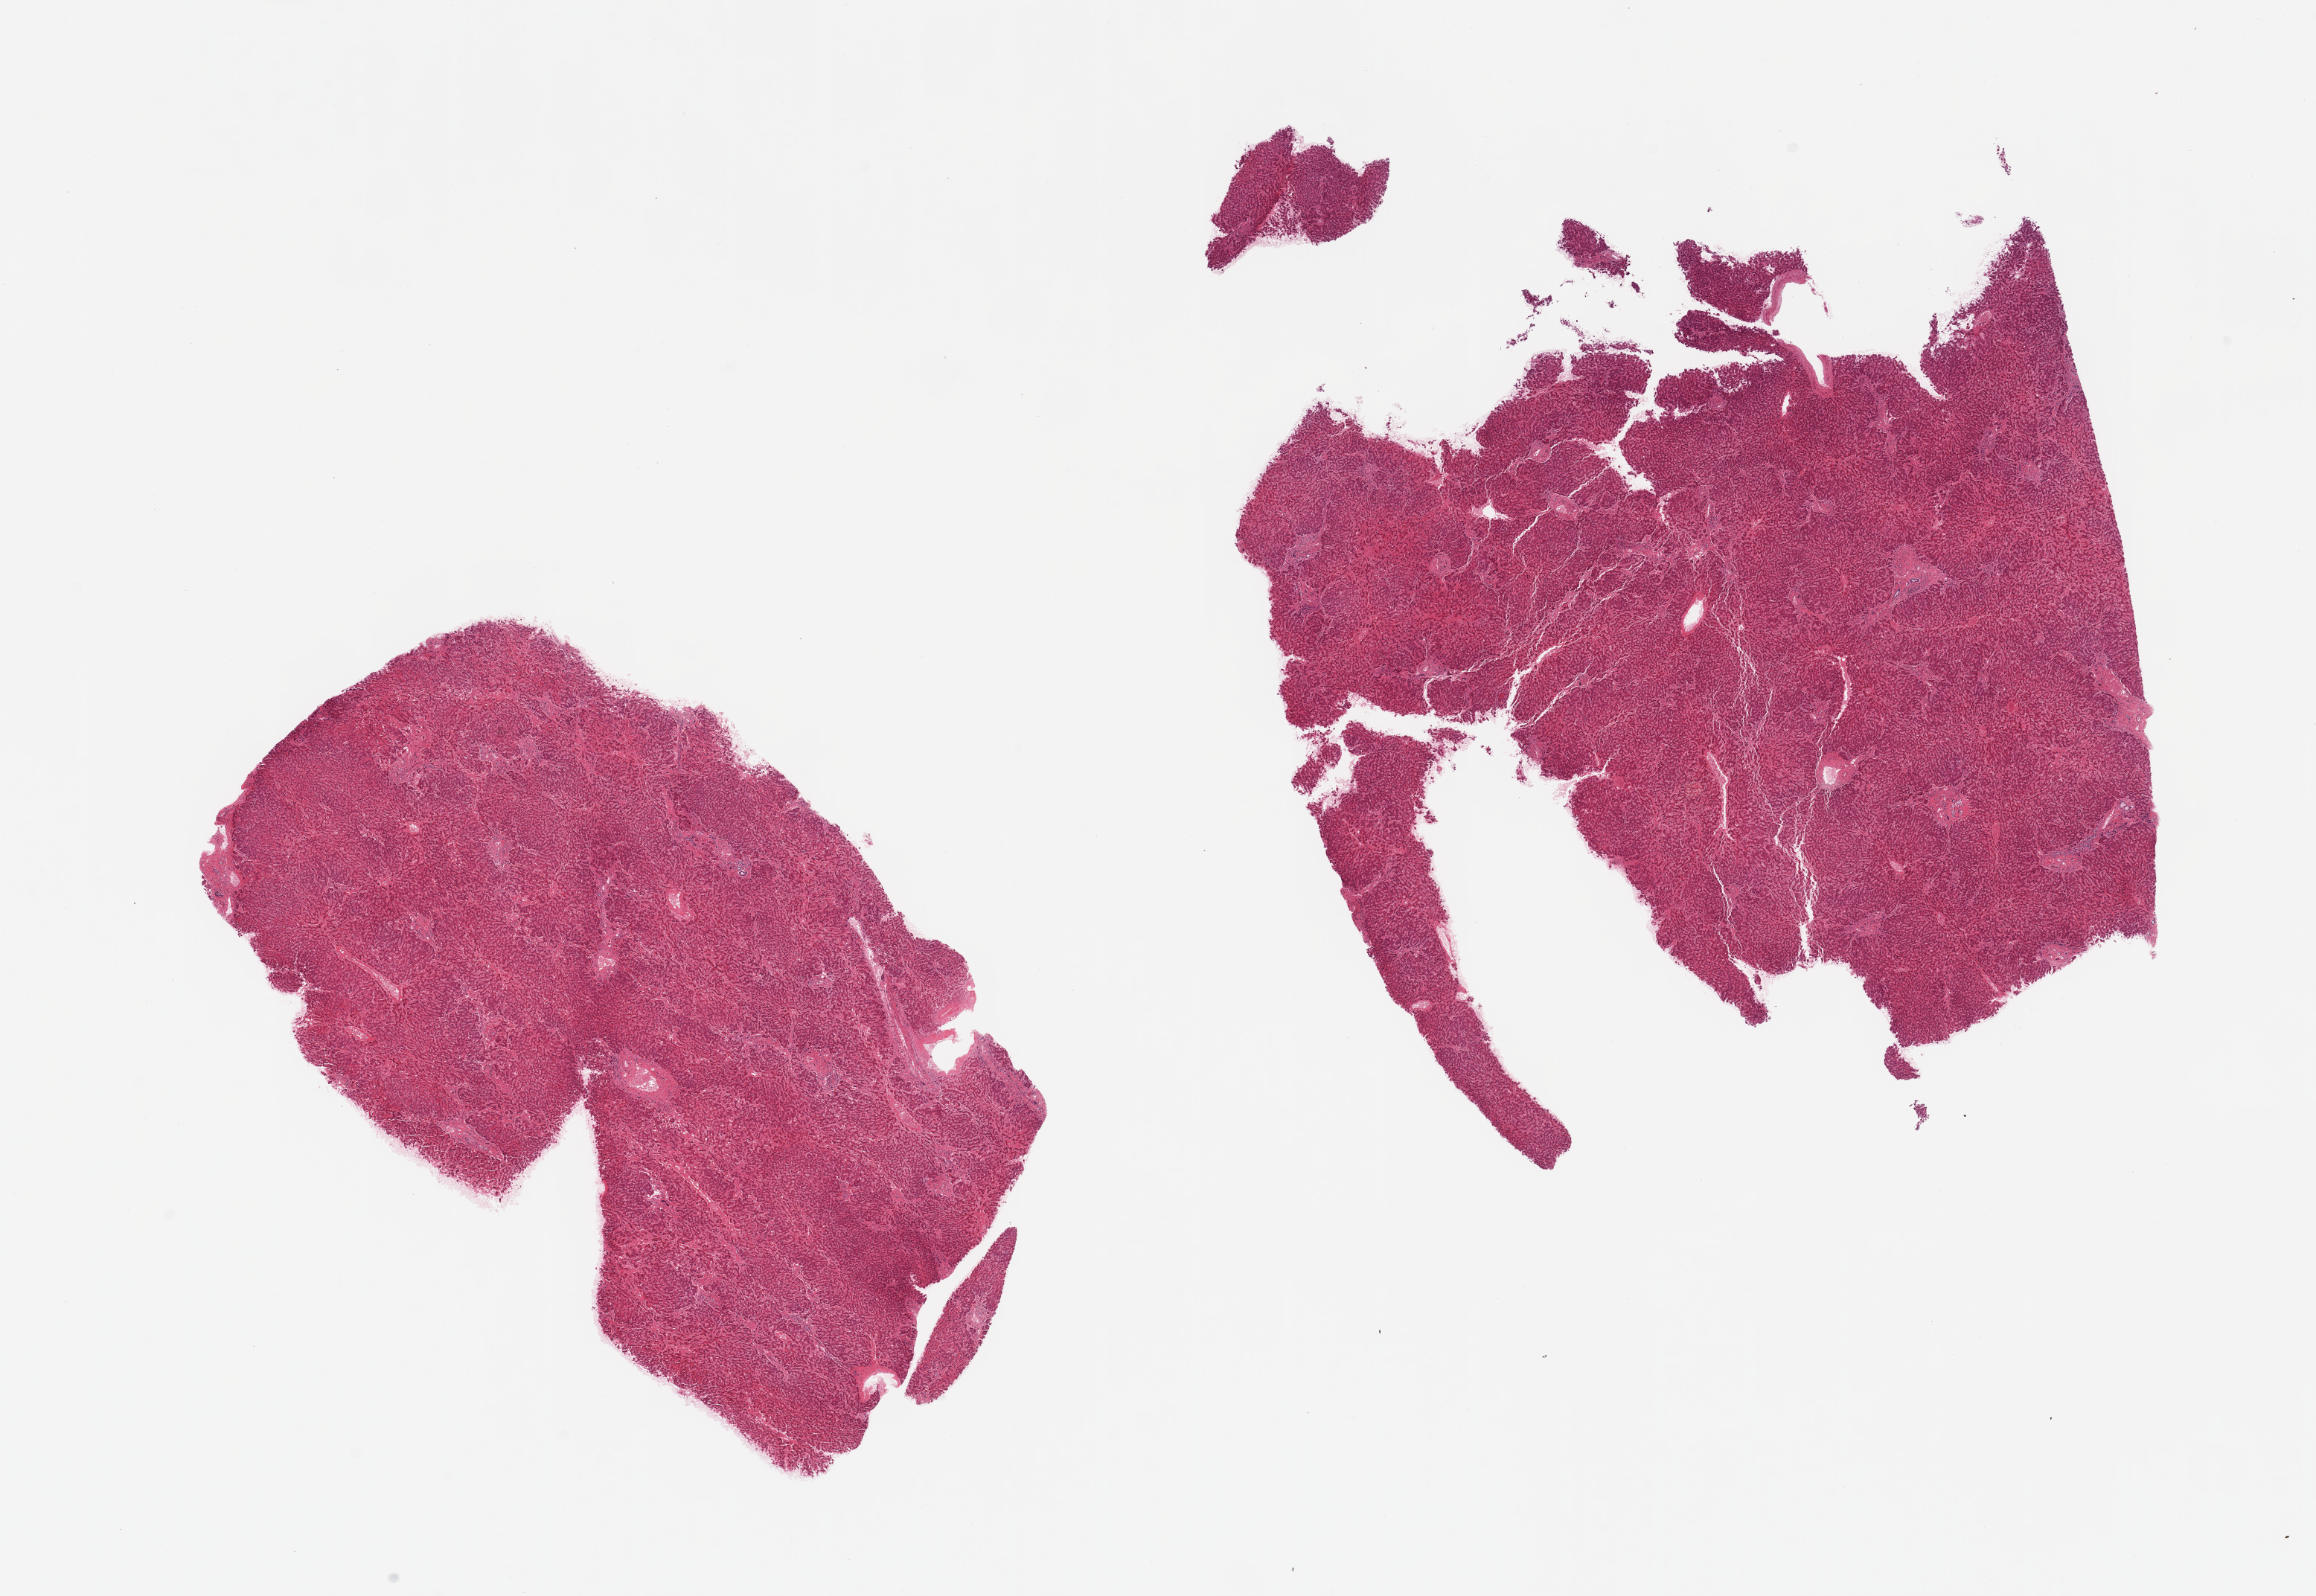
Whole-slide image, hematoxylin and eosin (H&E) stain, a low-resolution overview of the entire scanned area, about 24.6 x 17.0 mm (acquisition: 20x scan), PAXgene-fixed, paraffin-embedded tissue, section of liver (target tissue), donor tissue sample. Donor: male.
- reviewer comment on this tissue sample: 2 pieces; chronic passive congestion